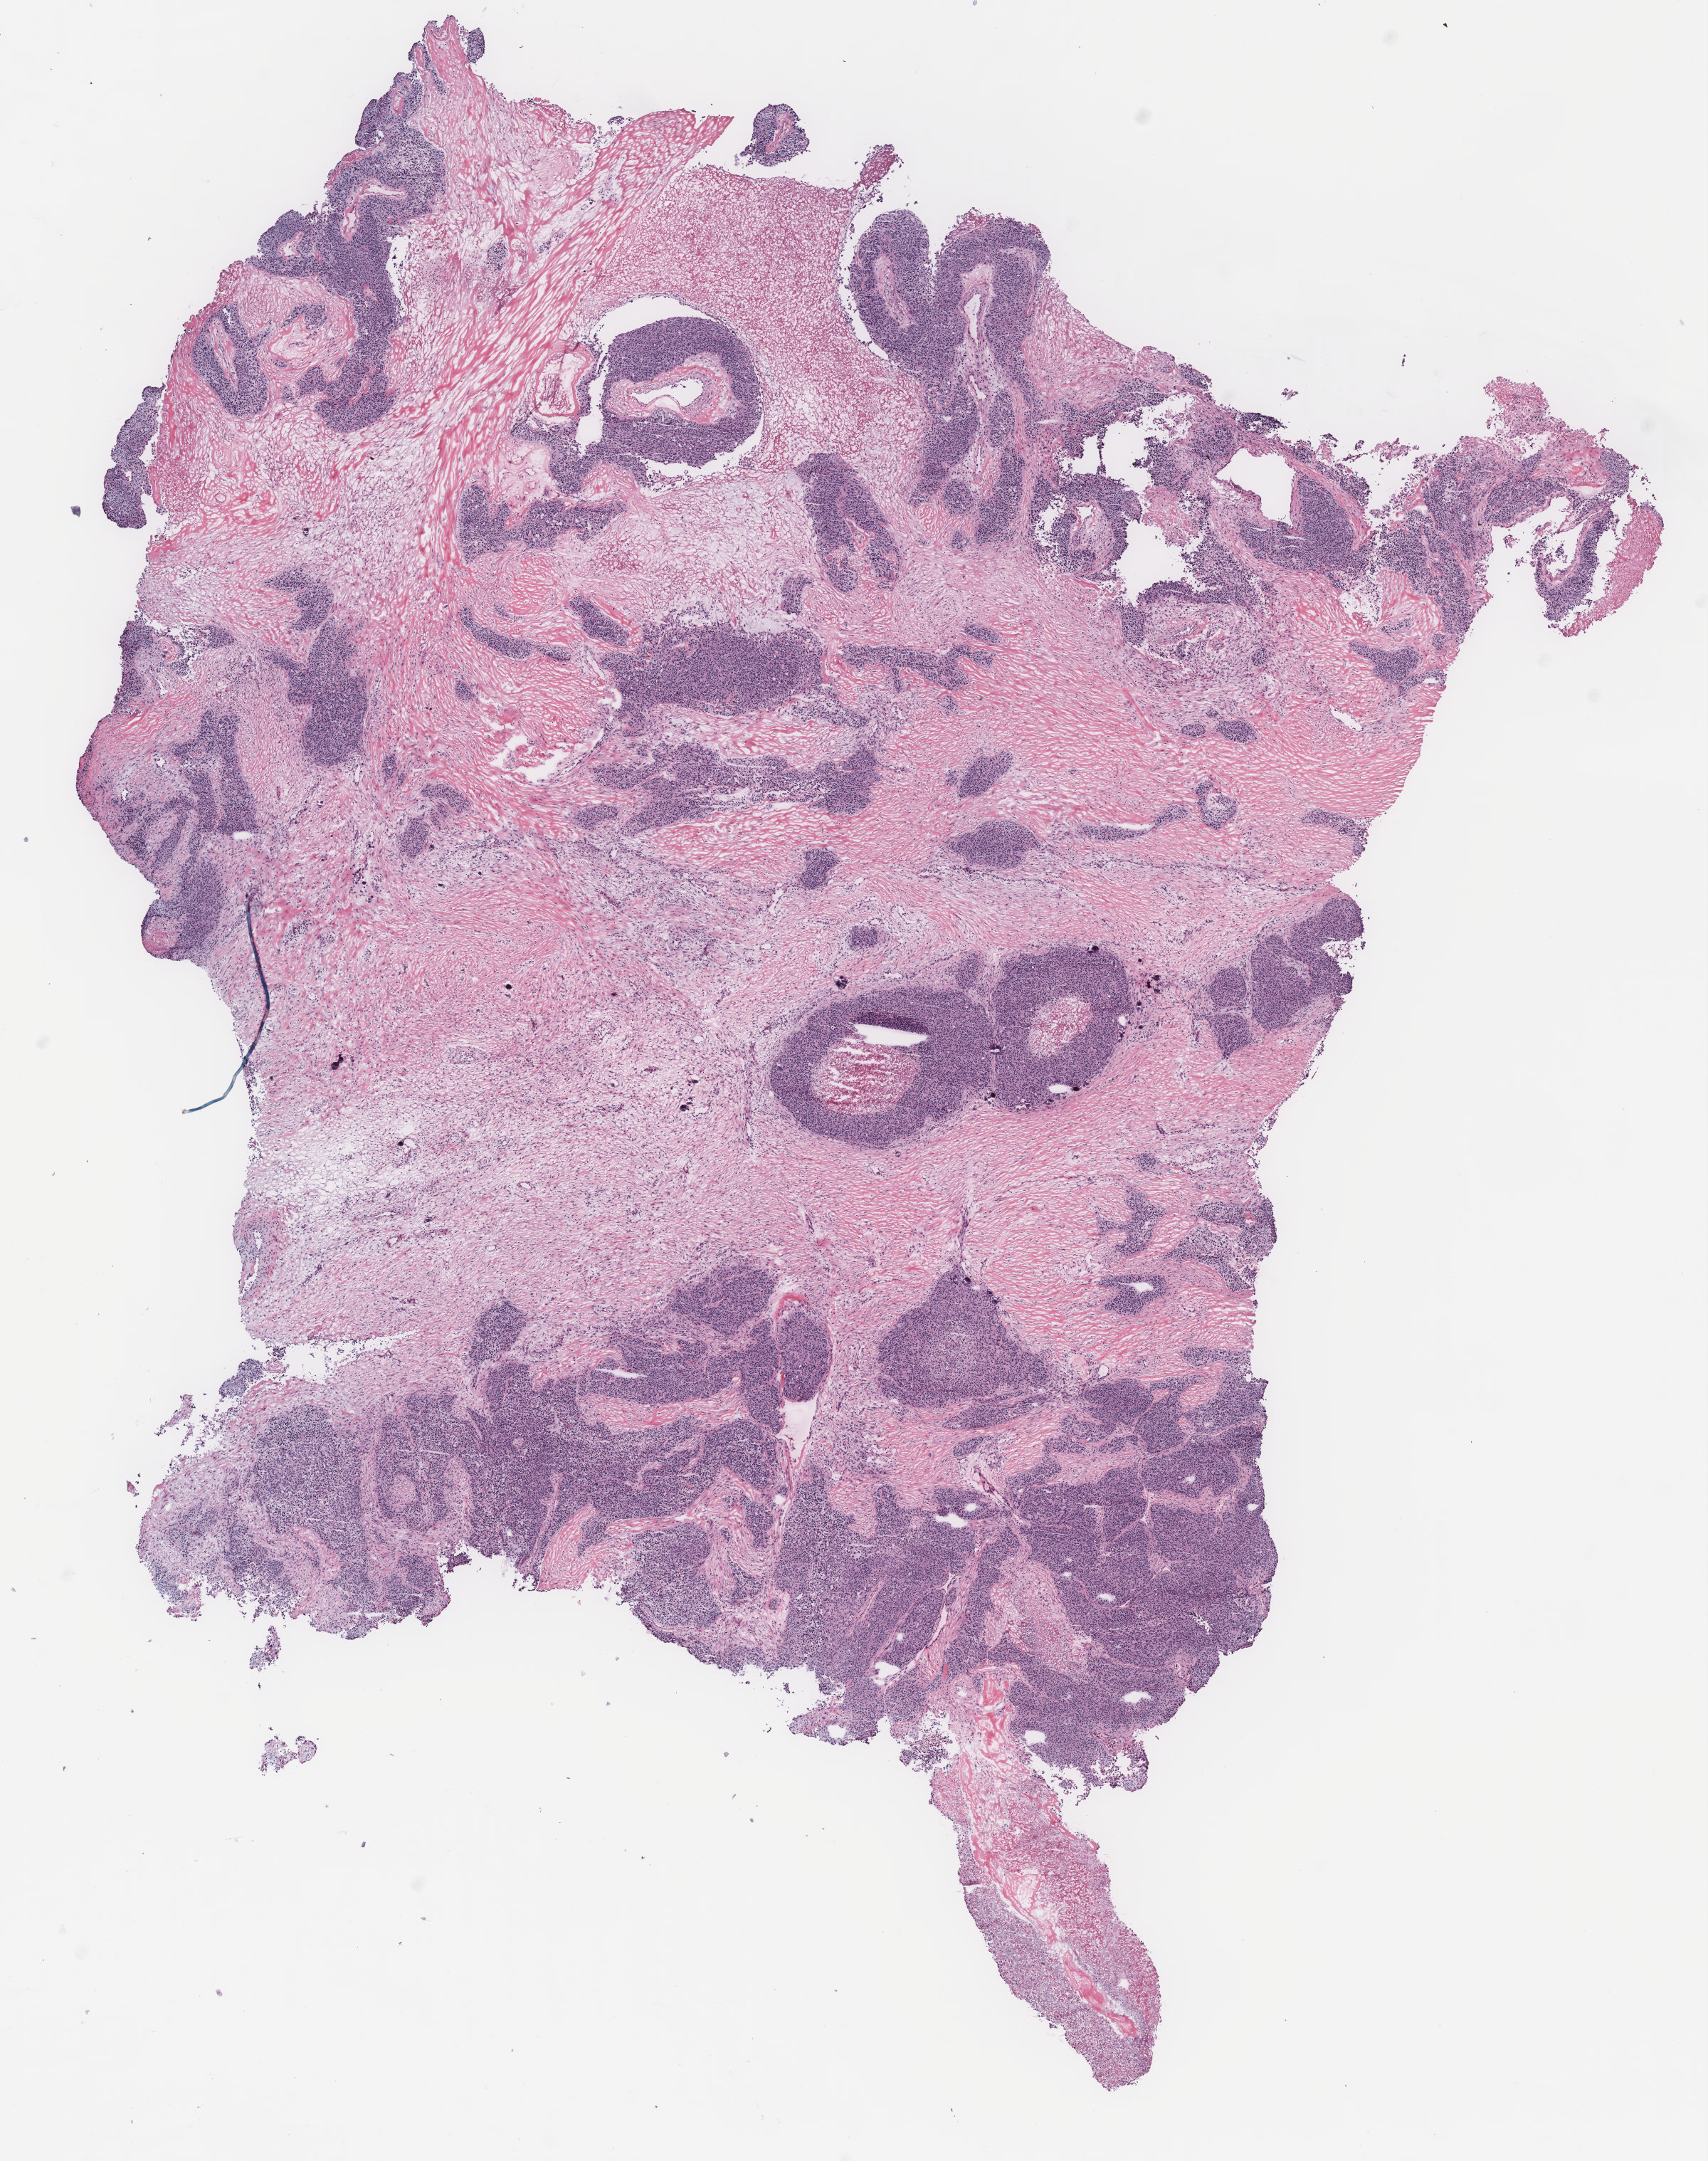
Whole-slide histology image, Hematoxylin and eosin (H&E) stained — whole scanned area (about 9.6 x 12.1 mm) shown as a low-resolution overview. Ovary, tissue type not recorded. Female patient.
Patient diagnosis: Serous adenocarcinoma, NOS.